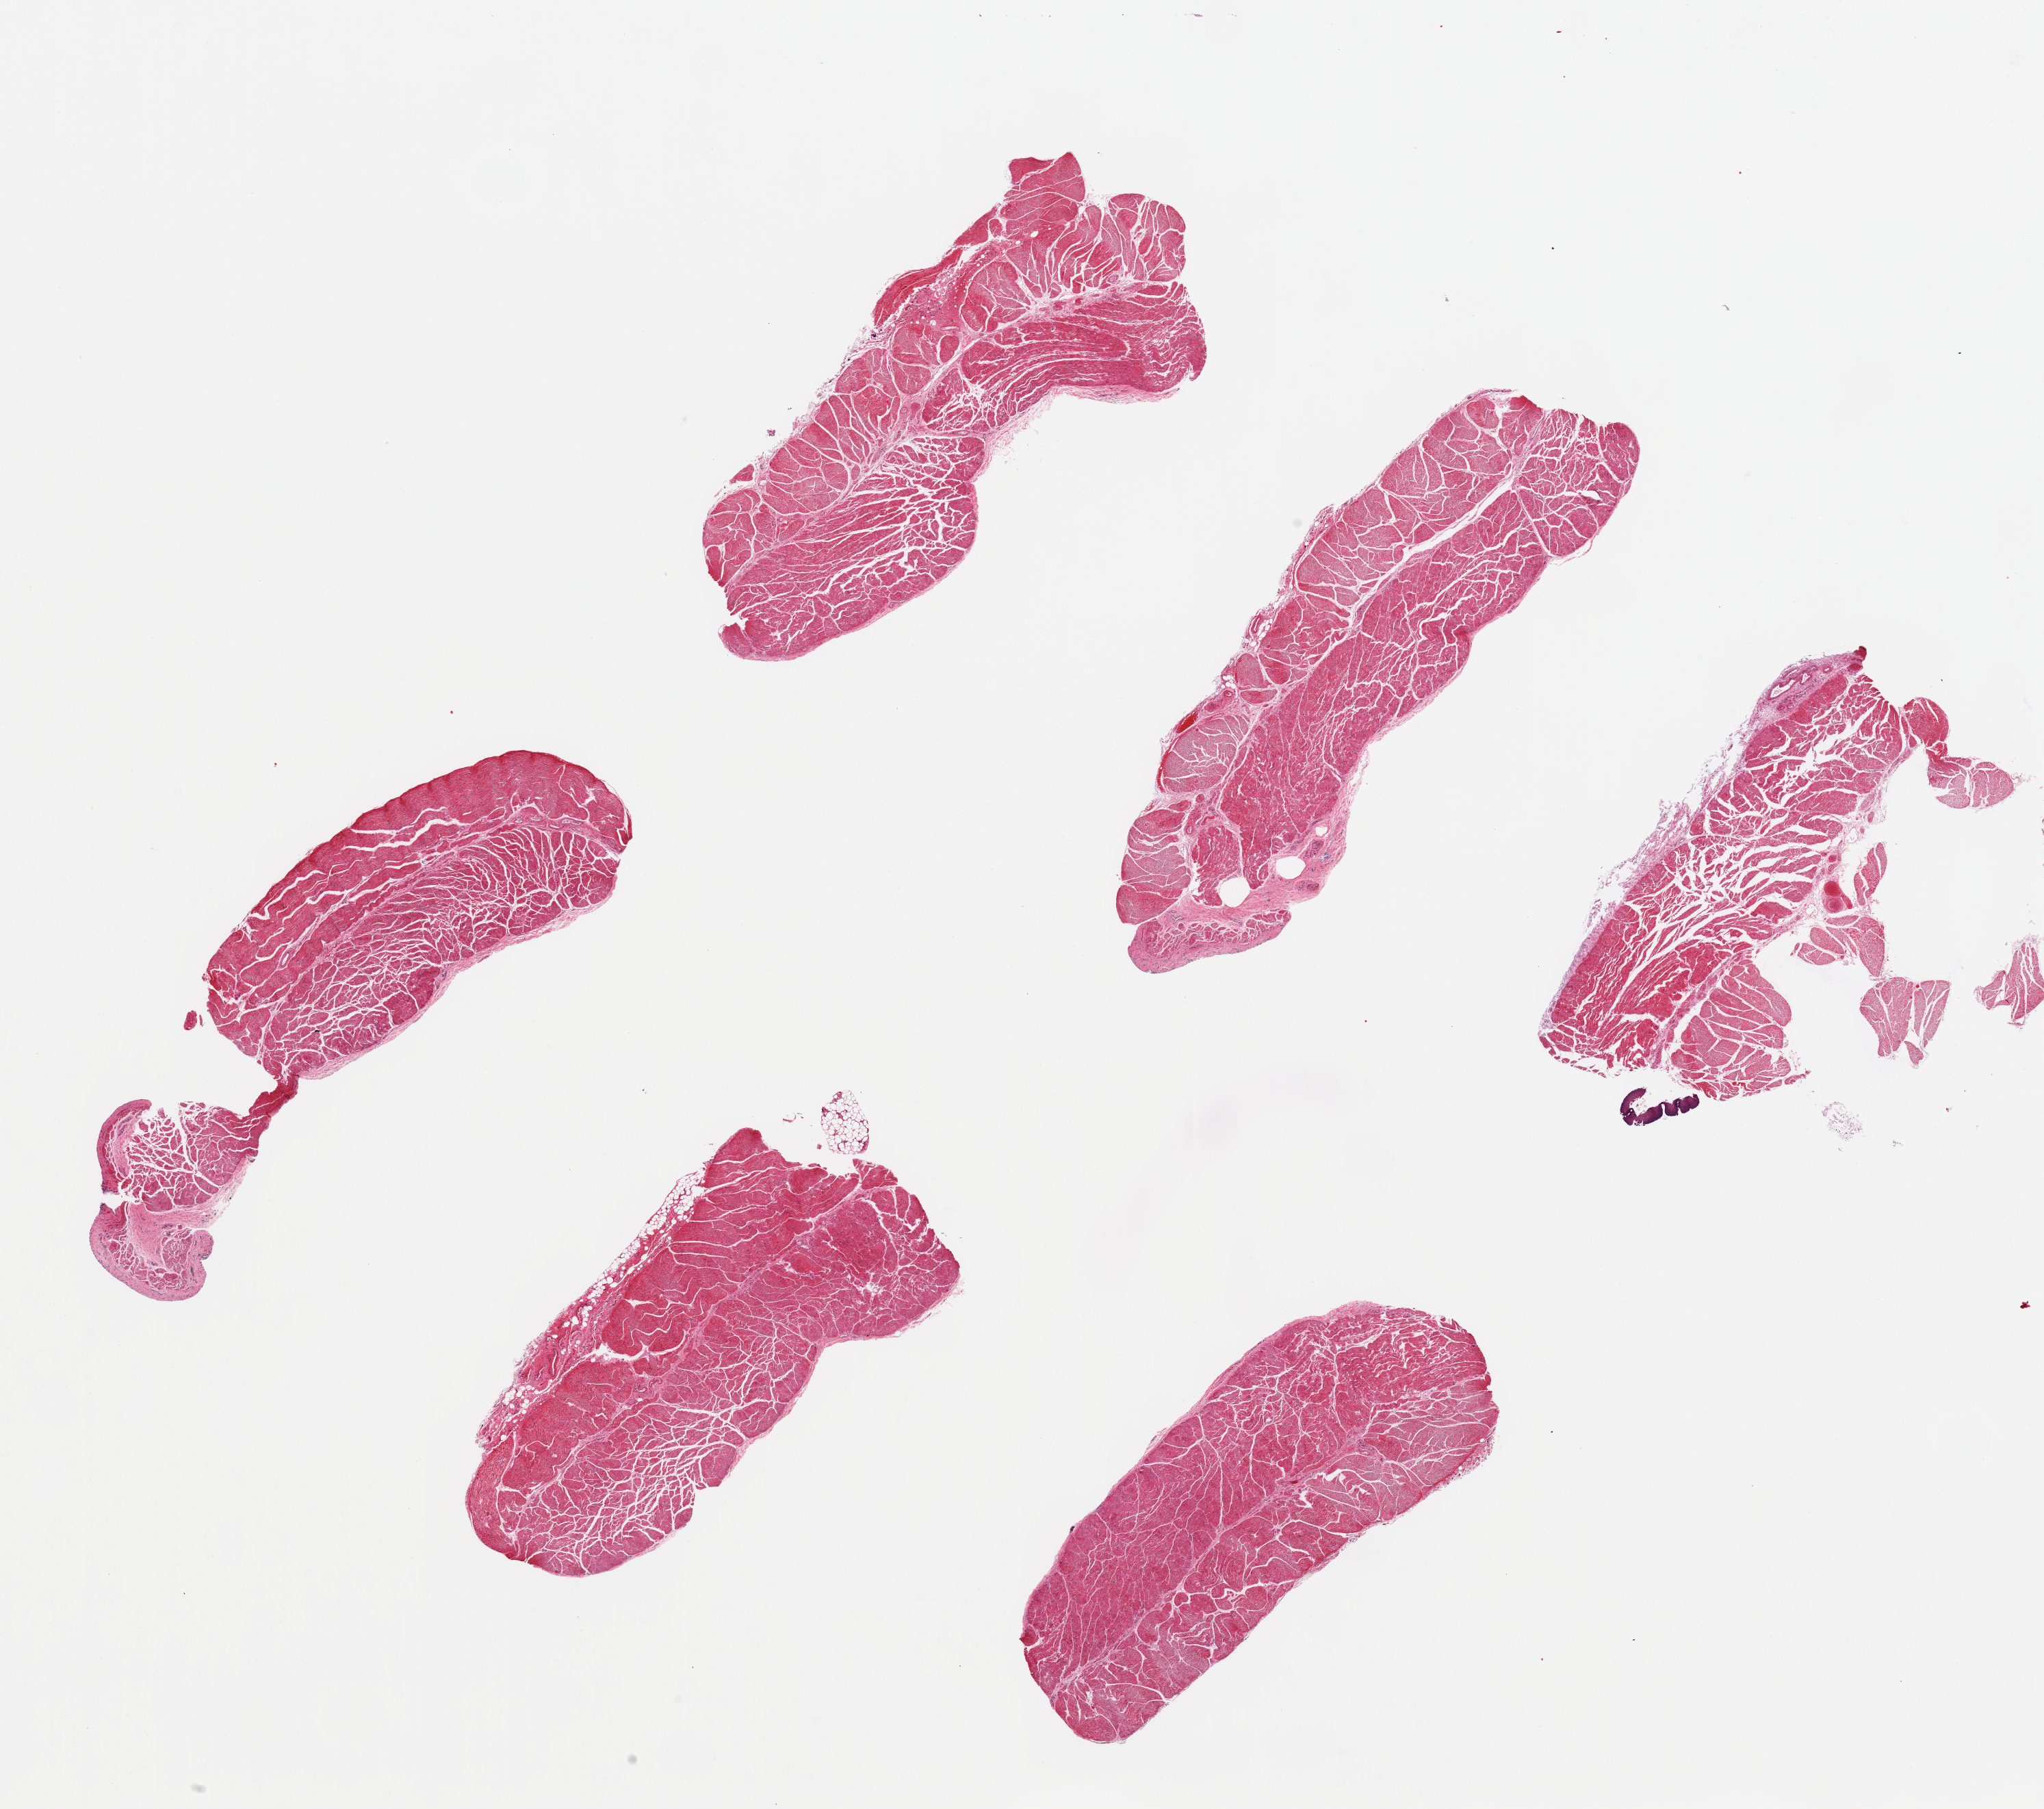
Whole-slide image, haematoxylin and eosin stain — a low-resolution overview of the entire scanned area, about 23.6 x 20.9 mm, PAXgene-fixed, paraffin-embedded tissue, target tissue: esophageal muscle, tissue donor sample.
• review note (as recorded): 6 pieces, ~7x2.5mm